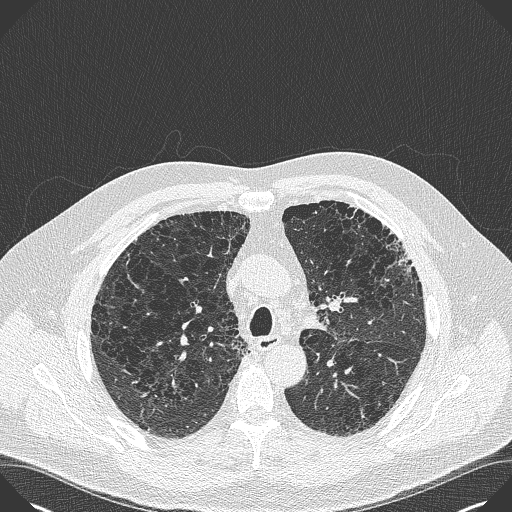
Low-dose screening chest CT, axial slice; baseline screening round; lung window (W 1500 / L -600 HU); 1 mm slice thickness; lung (sharp) reconstruction kernel (B50f); slice 126 of 383 in the series; 512 × 512 image matrix. Male participant, aged 59 years at enrolment. Current smoker at enrolment.
Expert reader's lesion annotation, bounding box [x1, y1, x2, y2] px = [376, 235, 426, 286]. Screening reader's record for this exam: no non-calcified nodule ≥4 mm recorded. Lung cancer was diagnosed 909 days after this screen: bronchiolo-alveolar carcinoma, mixed mucinous and non-mucinous, left upper lobe, stage IA (AJCC 6th edition), 20 mm at pathology.